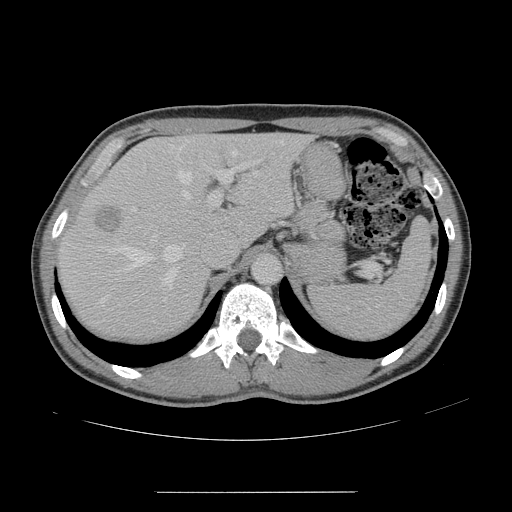
Contrast-enhanced abdominal CT, one axial slice. Slice 108 of 178 in the series (ordered by position). 120 kVp. Intravenous contrast given. Soft-tissue window (W 400 / L 40 HU). 2.5 mm slice thickness. 512 × 512 image matrix, field of view 401 × 401 mm. Male patient, age 53 years. From the clinical record (not read from this slice): diagnosis: colorectal cancer liver metastases, imaged before liver resection; multiple liver metastases: yes; largest metastasis: 2.4 cm; disease in both lobes: no.
Structures marked on this image (manually delineated by an expert):
- hepatic veins: bounding box <101,141,283,302> (left, top, right, bottom; pixels)
- liver: <61,135,305,338>
- planned liver remnant (the part of the liver to remain after resection): <148,135,305,242>
- portal vein (with intrahepatic branches): <132,159,261,241>
- liver metastasis: <94,207,124,235>